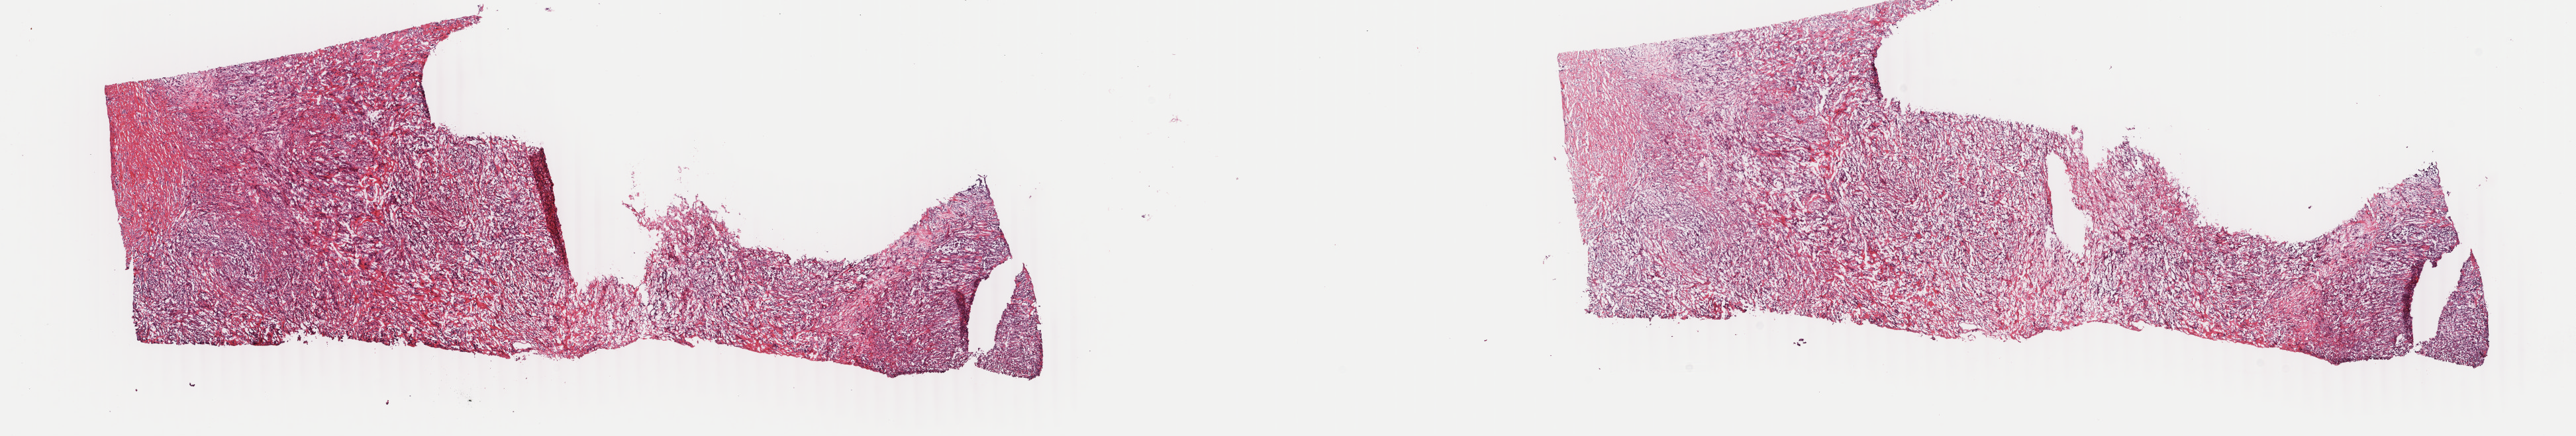
Digitized H&E tissue section (whole slide) — whole scanned area (about 30.9 x 5.2 mm, slide scanned at 40x) shown as a low-resolution overview. Frozen section. Mesothelium, primary tumour sample. Male patient; age at initial diagnosis 61 years. Pathologist review of this section (percent, as recorded): tumour cells 40%, tumour nuclei 80%, normal cells 0%, stromal cells 60%, necrosis 0%. Inflammatory infiltration, as recorded: lymphocyte infiltration 1%, monocyte infiltration 2%, neutrophil infiltration 0%.
AJCC pathologic stage: III (6th edition). Diagnosis: Epithelioid mesothelioma, malignant.